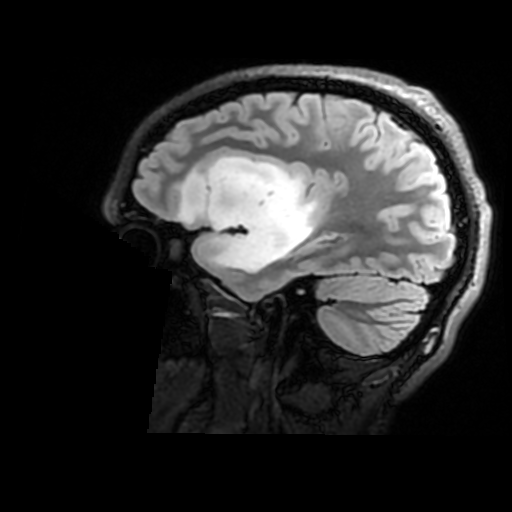
Brain MRI from a brain-tumour surgery series, one sagittal slice. Slice 124 of 176 in the series (ordered by position). T2 FLAIR. 512 × 512 image matrix, field of view 240 × 240 mm. From the clinical record (not read from this slice): histopathology: Astrocytoma; WHO grade: 2; IDH mutation: yes; tumour location: Right Insular.
Annotated regions visible in this slice (manually delineated by an expert):
- tumour: box from (x=179, y=156) to (x=320, y=275) px